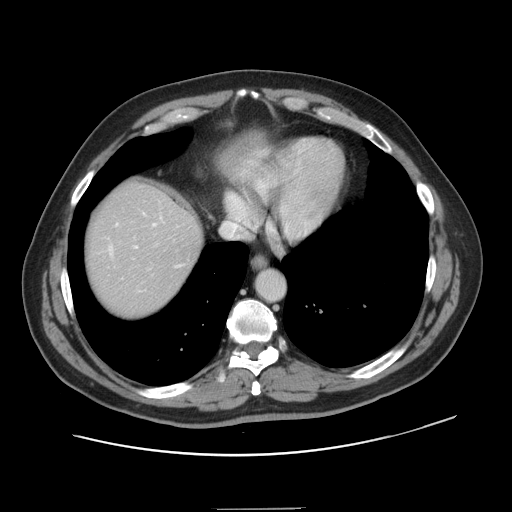
Contrast-enhanced abdominal CT, one axial slice. Position 131 of 143 along the scan axis. Intravenous contrast given. Soft-tissue window (W 400 / L 40 HU). 512 × 512 image matrix, field of view 402 × 402 mm. Male patient, age 62 years. From the clinical record (not read from this slice): diagnosis: colorectal cancer liver metastases, imaged before liver resection; multiple liver metastases: yes; largest metastasis: 2.7 cm; disease in both lobes: no.
Structures marked on this image (expert manual segmentation):
- hepatic veins: bounding box (x1, y1, x2, y2) in pixels: (116, 216, 180, 267)
- liver: (86, 184, 202, 317)
- planned liver remnant (the part of the liver to remain after resection): (86, 184, 202, 301)